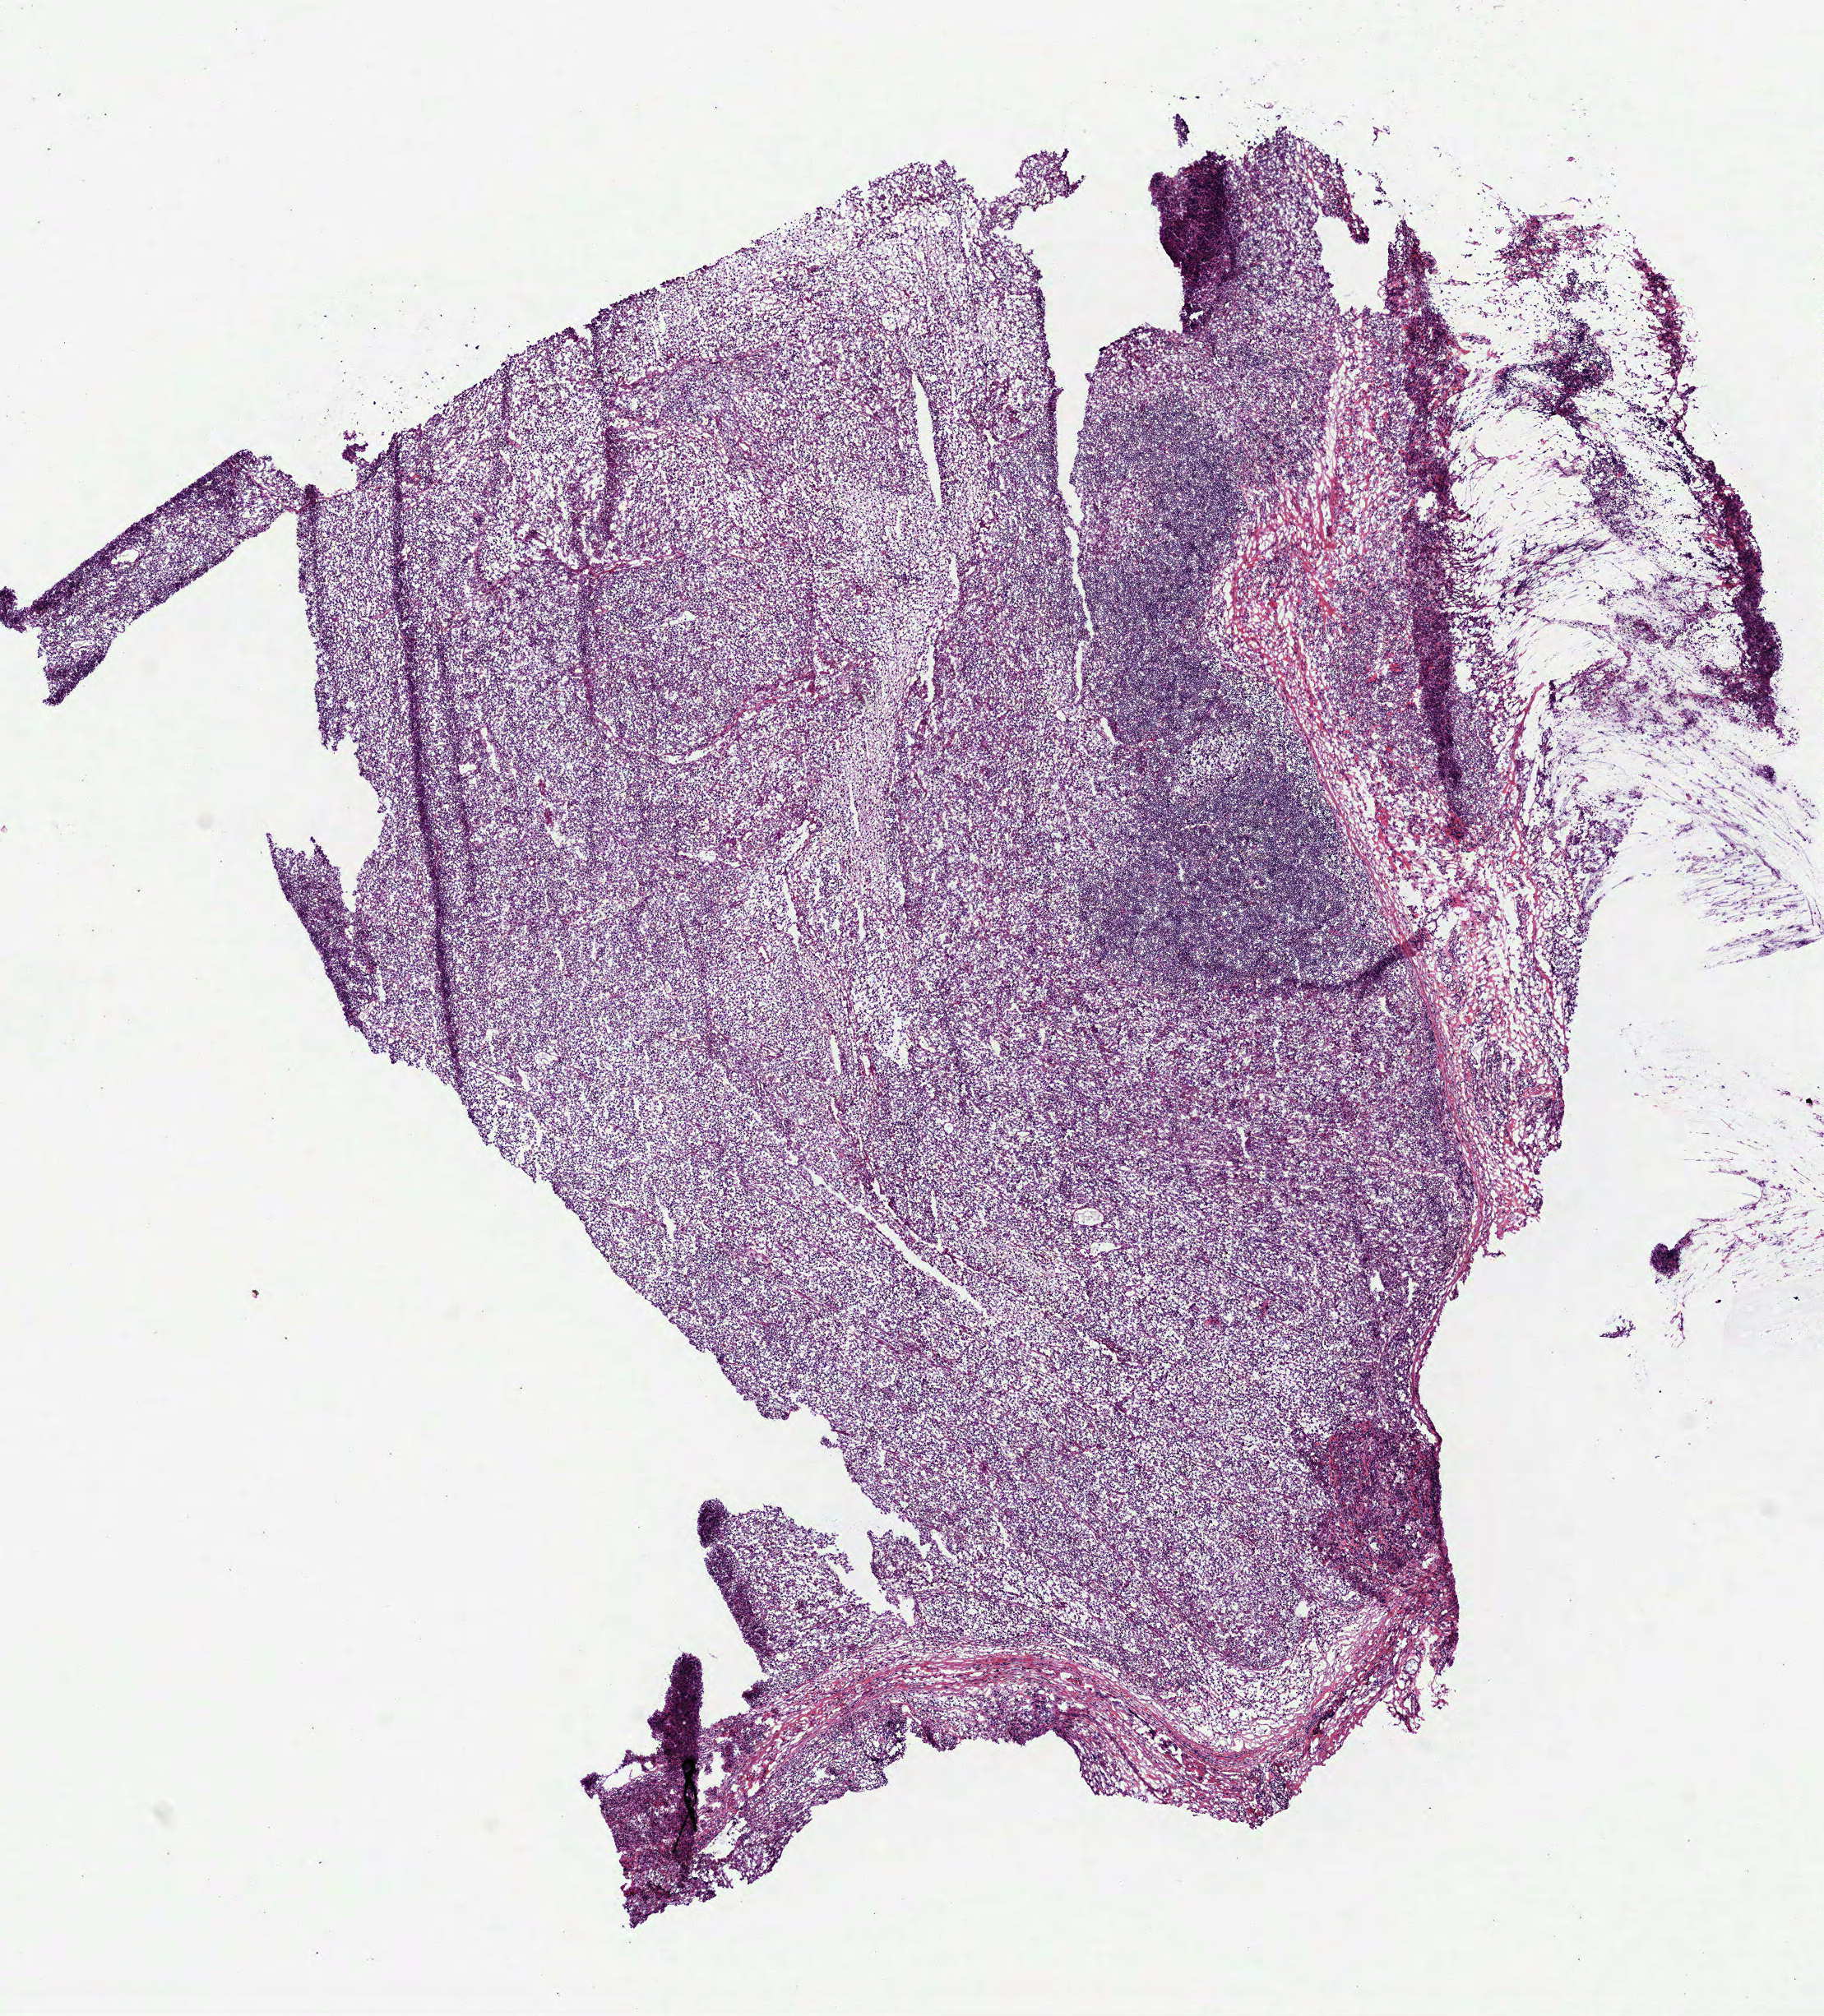
Whole-slide histology image, H&E, low-resolution overview of the scanned area, about 8.9 x 9.9 mm (from a 40x scan); frozen section from the bottom of the tissue portion; sample: primary tumour, lymphoid tissue. Male patient; age at initial diagnosis 51 years. Slide review estimates, as recorded: tumour cells 85%, tumour nuclei 80%, normal cells 14%, stromal cells 0%, necrosis 1%. Infiltration values recorded for this section: lymphocyte infiltration 18%, monocyte infiltration 0%, neutrophil infiltration 0%.
- diagnosis: Diffuse large B-cell lymphoma, NOS (submandibular gland)